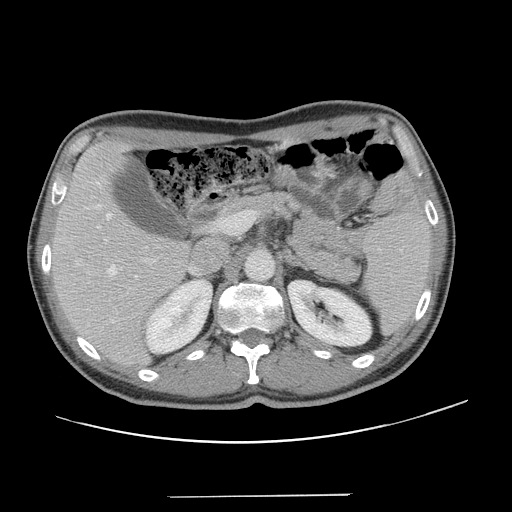
Contrast-enhanced abdominal CT, one axial slice. 120 kVp. Soft-tissue window (W 400 / L 40 HU). 2.5 mm slice thickness. 512 × 512 image matrix, field of view 403 × 403 mm. Male patient, age 60 years. From the clinical record (not read from this slice): diagnosis: colorectal cancer liver metastases, imaged before liver resection; multiple liver metastases: no; largest metastasis: 2.5 cm; disease in both lobes: no.
Annotated regions visible in this slice (outlined manually by an expert reader):
- hepatic veins: bounding box <98,205,137,277> (left, top, right, bottom; pixels)
- liver: <52,142,187,365>
- planned liver remnant (the part of the liver to remain after resection): <52,142,187,359>
- portal vein (with intrahepatic branches): <152,260,154,263>